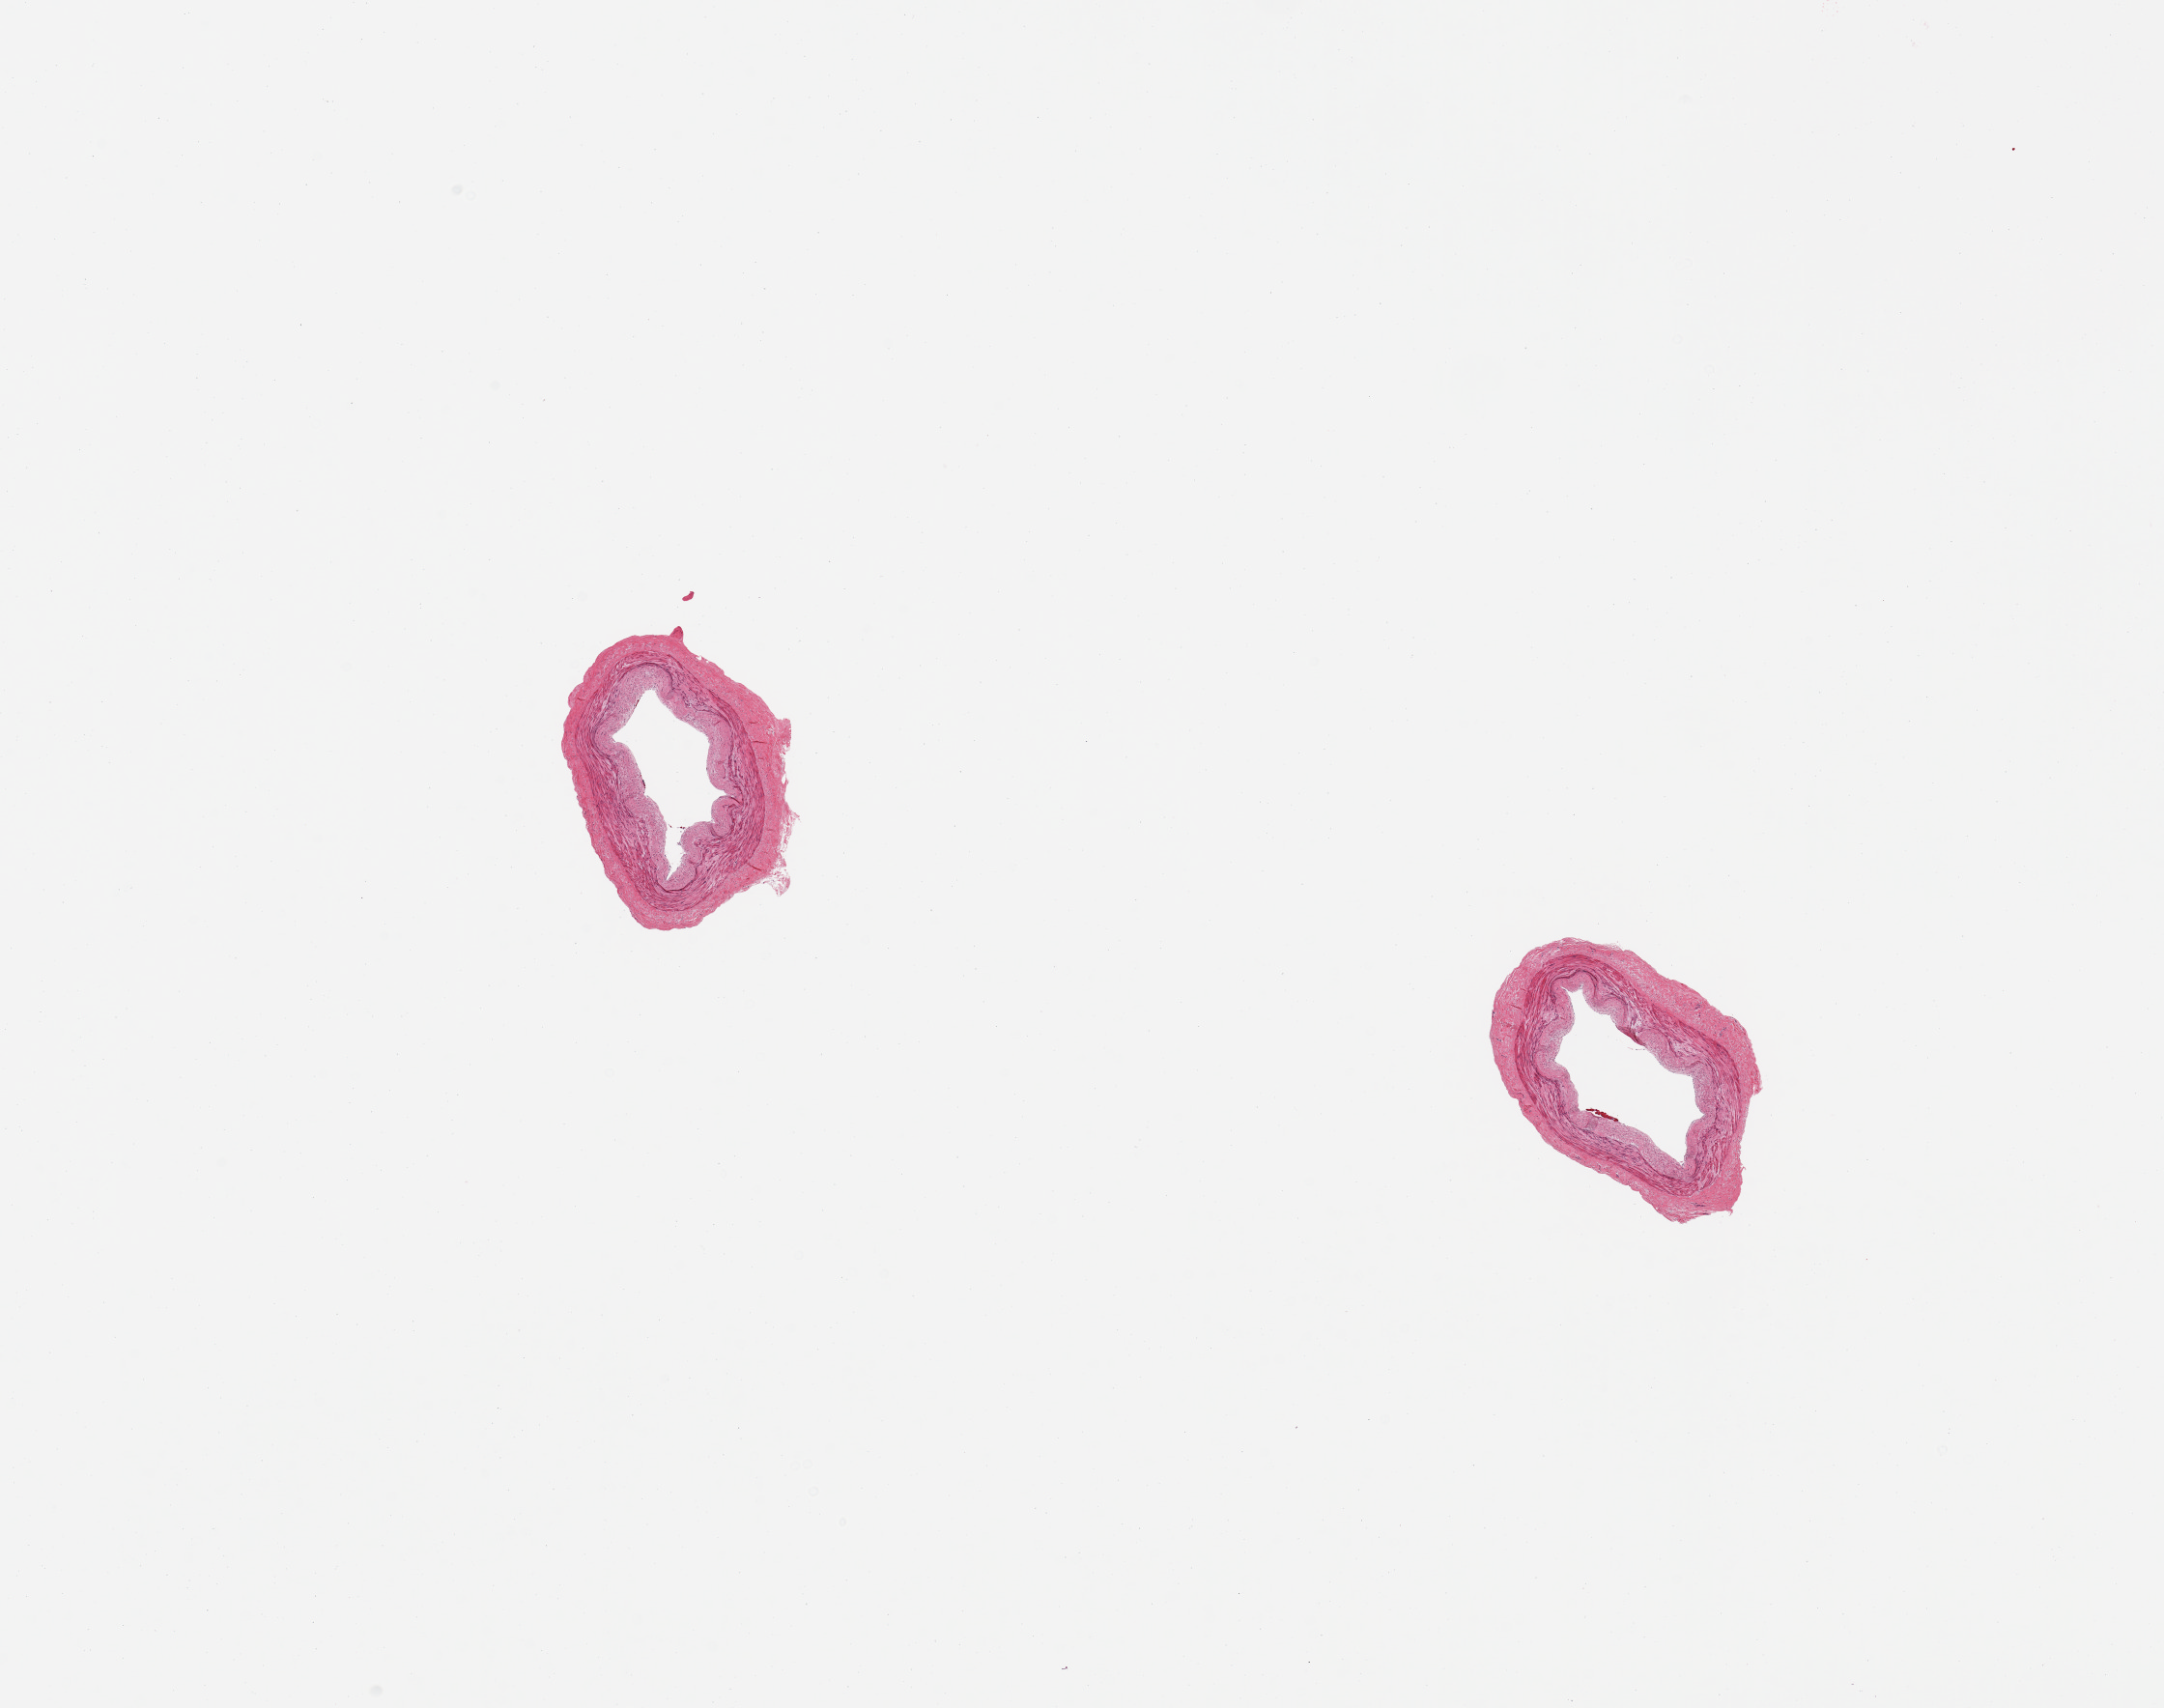
Digitized H&E-stained section, low-resolution overview of the scanned area, about 17.7 x 14.0 mm (slide scanned at 20x). PAXgene-fixed, paraffin-embedded tissue. Target tissue: tibial artery. Tissue donor sample. Male donor.
Reviewer comment on this tissue sample: 2 pieces; well dissected; no lesions.